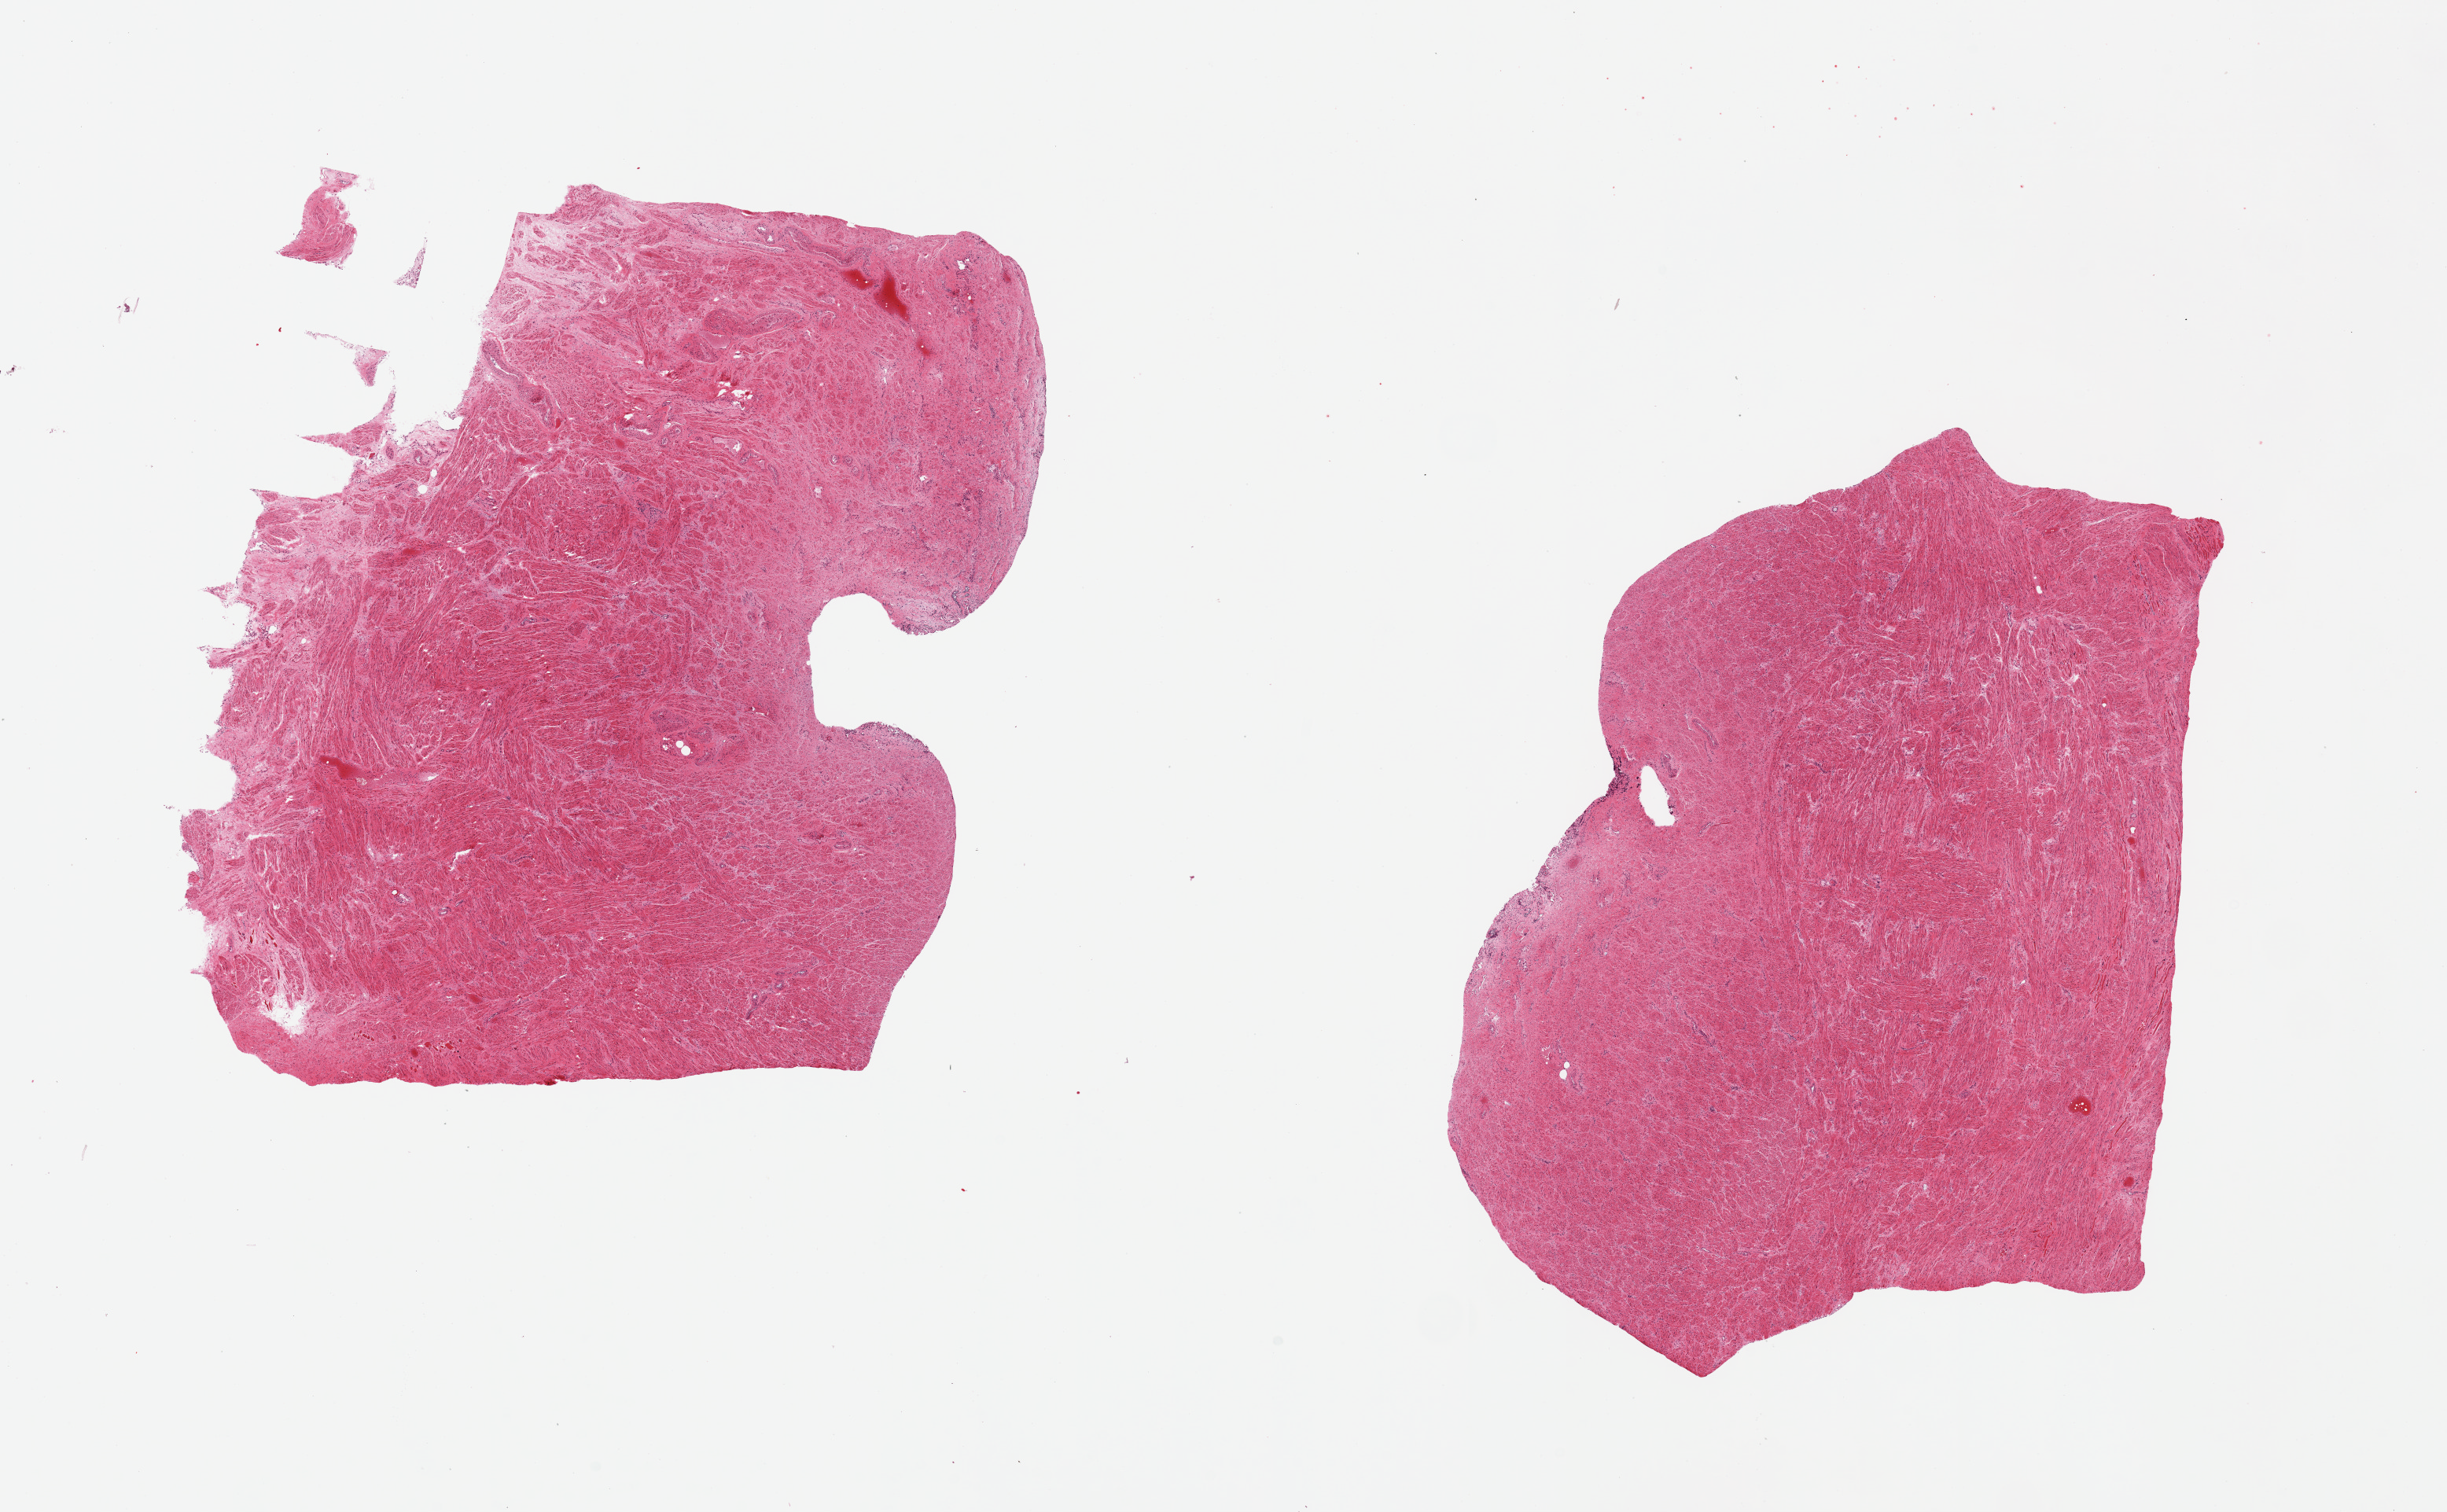
Digitized H&E-stained section — low-resolution overview of the scanned area, about 24.6 x 15.2 mm (acquisition: 20x scan). PAXgene-fixed paraffin-embedded (PFPE) section. Section of prostate (target tissue). Donor tissue sample. Donor sex: male.
* review note (as recorded): 2 pieces. All smooth muscle; no glands